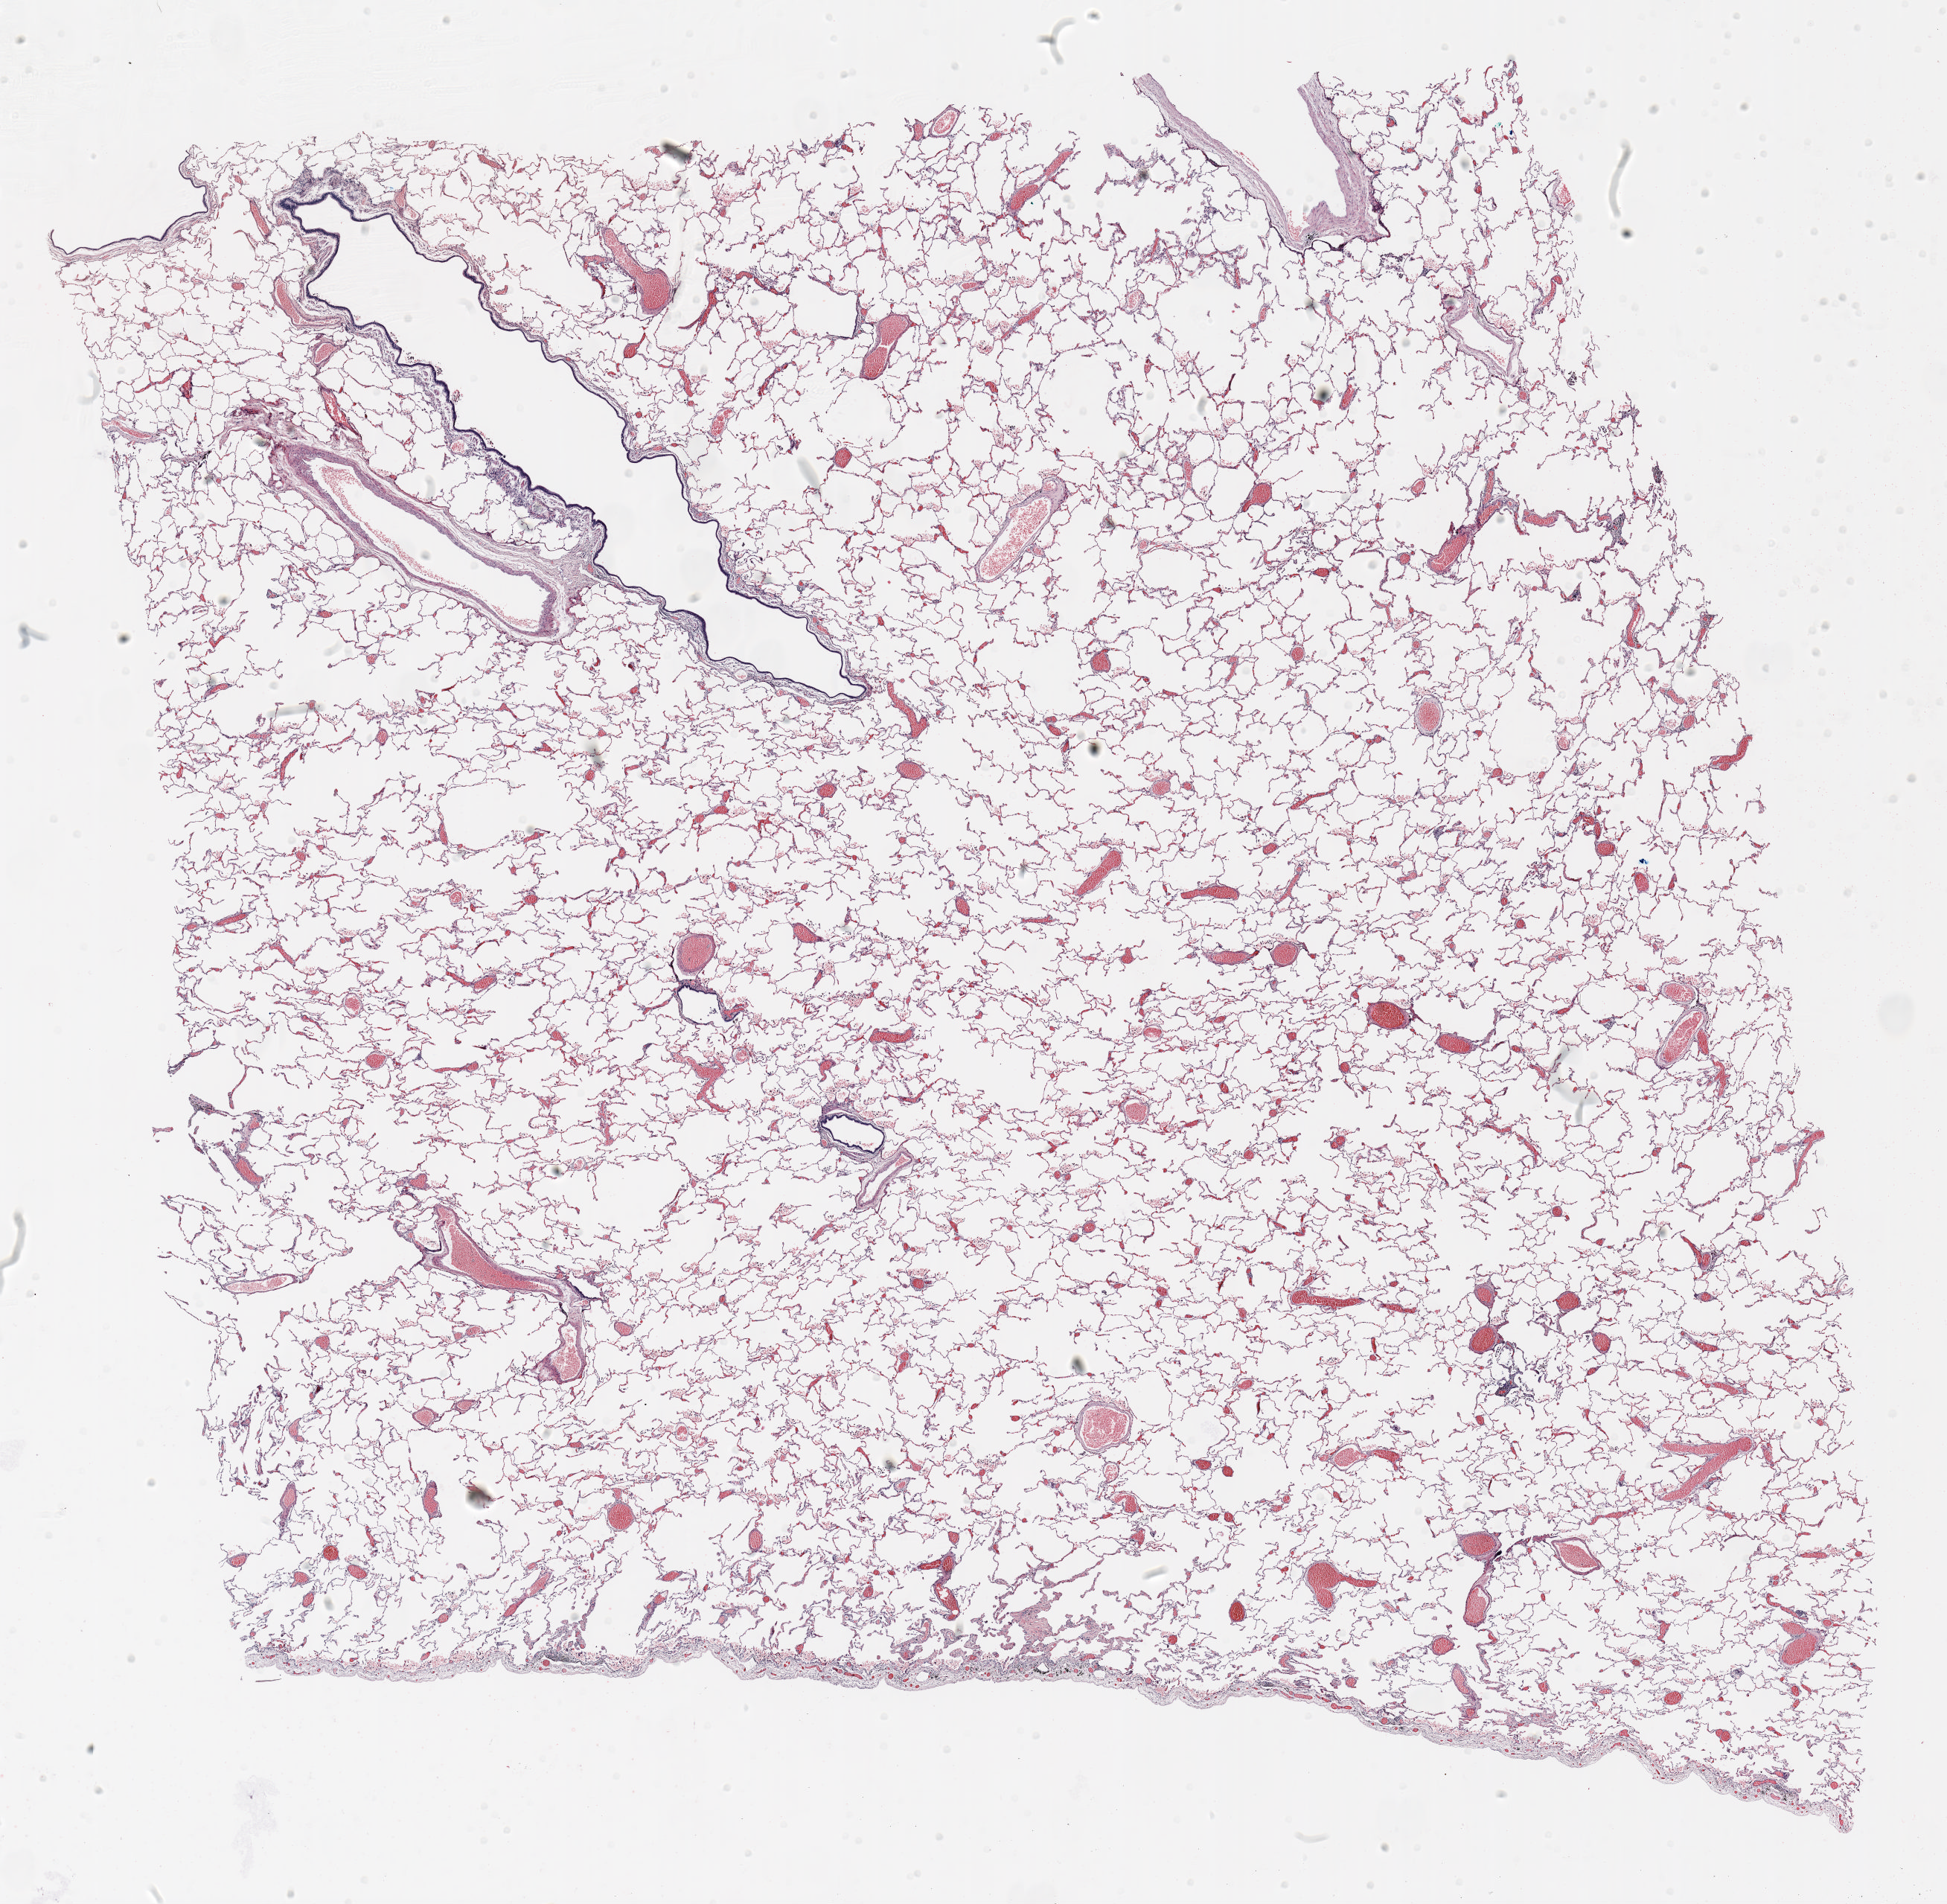
H&E whole-slide image — shown as a low-resolution overview of the whole scanned area (about 21.0 x 20.6 mm, acquisition: 20x scan); FFPE section; lung tissue. Male, age 65 at enrolment. Current smoker at enrolment. Grade: poorly differentiated (G3).
Tumour size (pathology): 18 mm. Primary tumour location (clinical record): right lower lobe. Participant's lung-cancer diagnosis: Adenocarcinoma, NOS. Stage (AJCC 6th edition): IA.